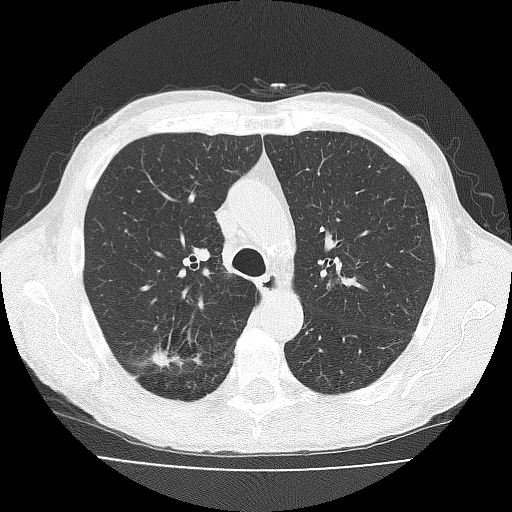
Axial slice from a low-dose chest CT screening exam, third annual screen, lung window (W 1500 / L -600 HU), 2 mm slice thickness, lung (sharp) reconstruction kernel (FC51), 120 kVp, slice 60 of 181 in the series. Male, age 73 years at enrolment. Current smoker at enrolment.
- Lesion marked by an expert reader, box from (x=140, y=329) to (x=191, y=378) px.
- The exam's reader record, not a measurement of the box and not confirmed to be the same lesion: non-calcified nodule or mass ≥4 mm, right upper lobe, 11 × 10 mm, spiculated (stellate) margins, soft tissue attenuation, pre-existing on the prior screen: no.
- Participant outcome: lung cancer diagnosed 38 days after this screen — adenosquamous carcinoma, right upper lobe, well differentiated (G1), stage IA (AJCC 6th edition), 20 mm at pathology.